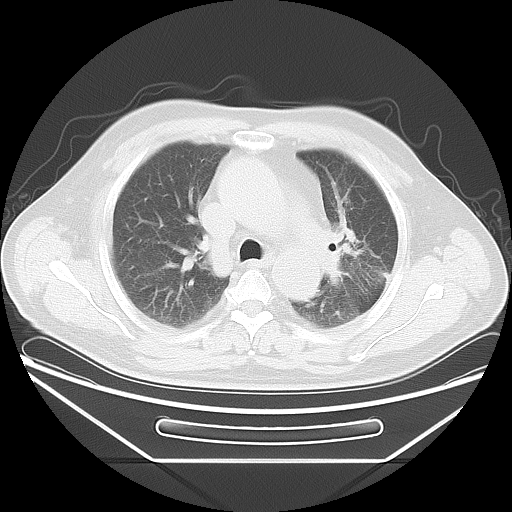
Chest CT, one axial slice; position 26 of 37 along the scan axis; reconstruction kernel LUNG; 120 kVp; lung window (W 1500 / L -600 HU); 5 mm slice thickness; 512 × 512 image matrix, field of view 411 × 411 mm. Patient: male, 61 years. Case-level facts recorded for this patient, not image findings: clinical TNM (as recorded): T2a N0 M0; histopathological grade: G3.
Outlined on this slice (bounding box drawn by a radiologist):
- lung tumour (recorded histology: small cell carcinoma): bounding box [x1, y1, x2, y2] px = [317, 183, 399, 301]